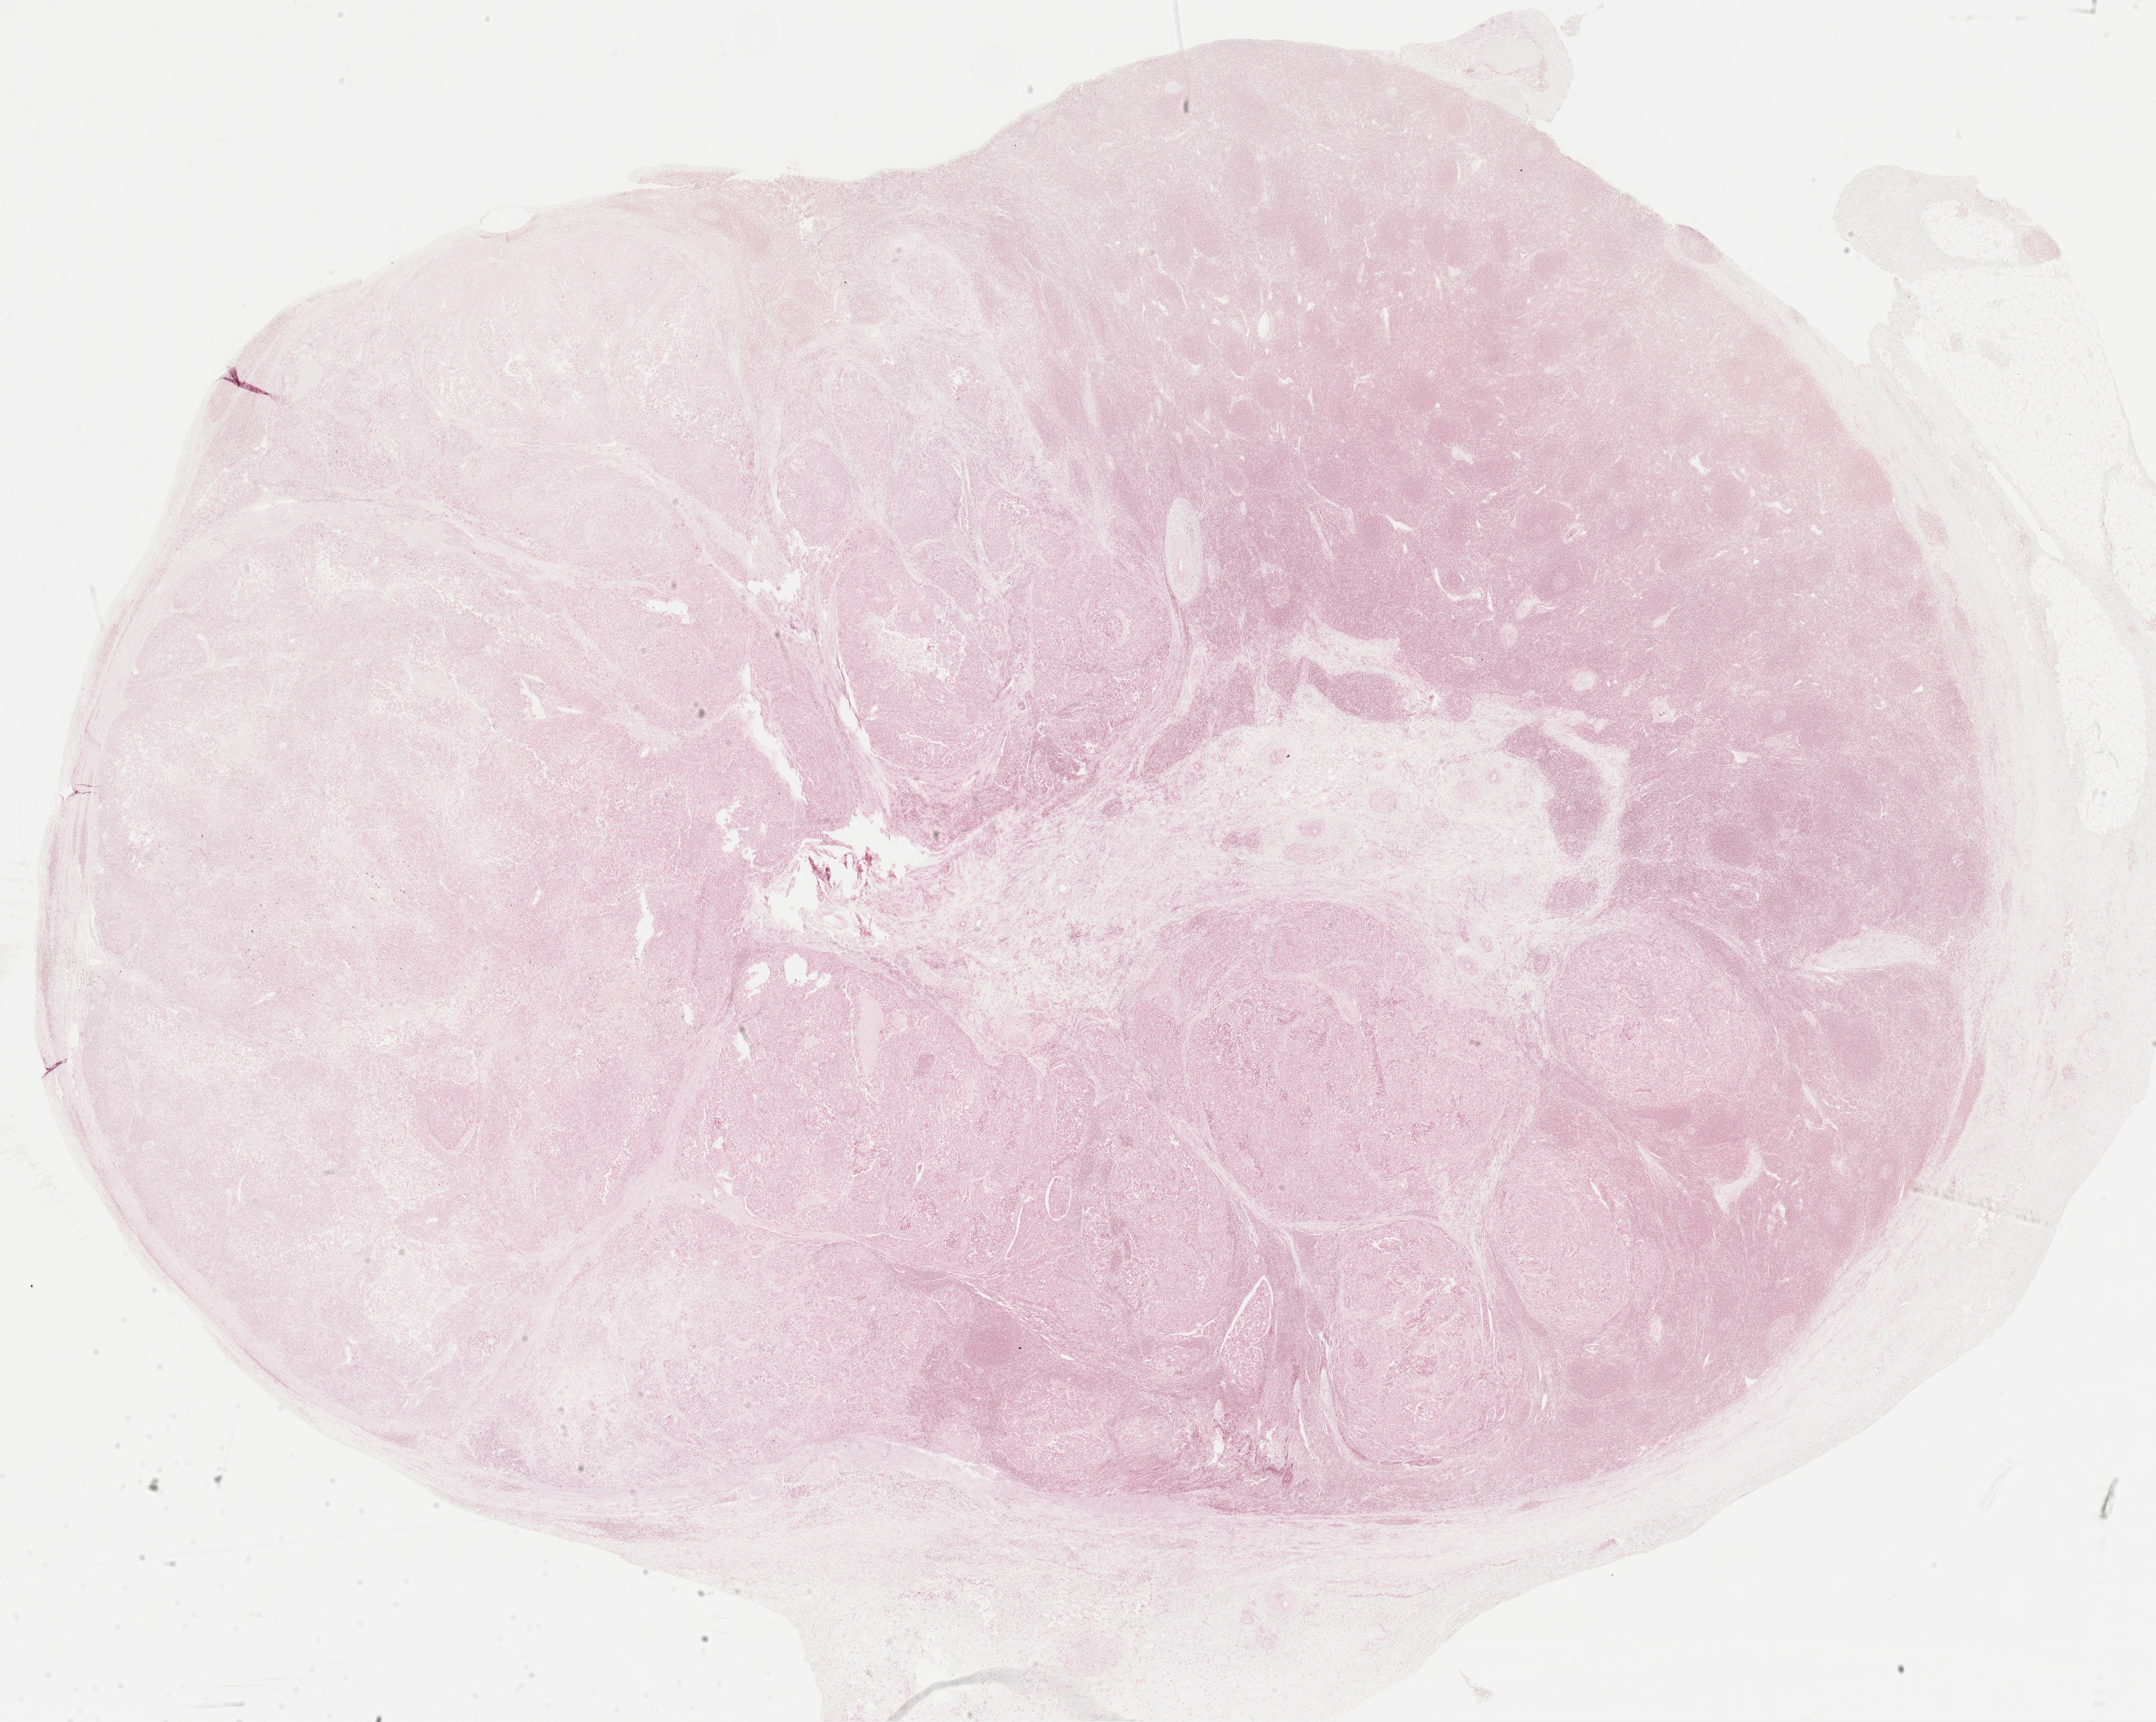
Hematoxylin and eosin (H&E) stained whole-slide image, low-resolution overview of the scanned area, about 23.6 x 18.8 mm, formalin-fixed paraffin-embedded (FFPE) diagnostic section, metastatic tumour sample, sampled site: lymph nodes of axilla or arm. Patient: female, age at initial diagnosis 46 years.
- this section: metastatic tumour tissue
- patient diagnosis: Malignant melanoma, NOS